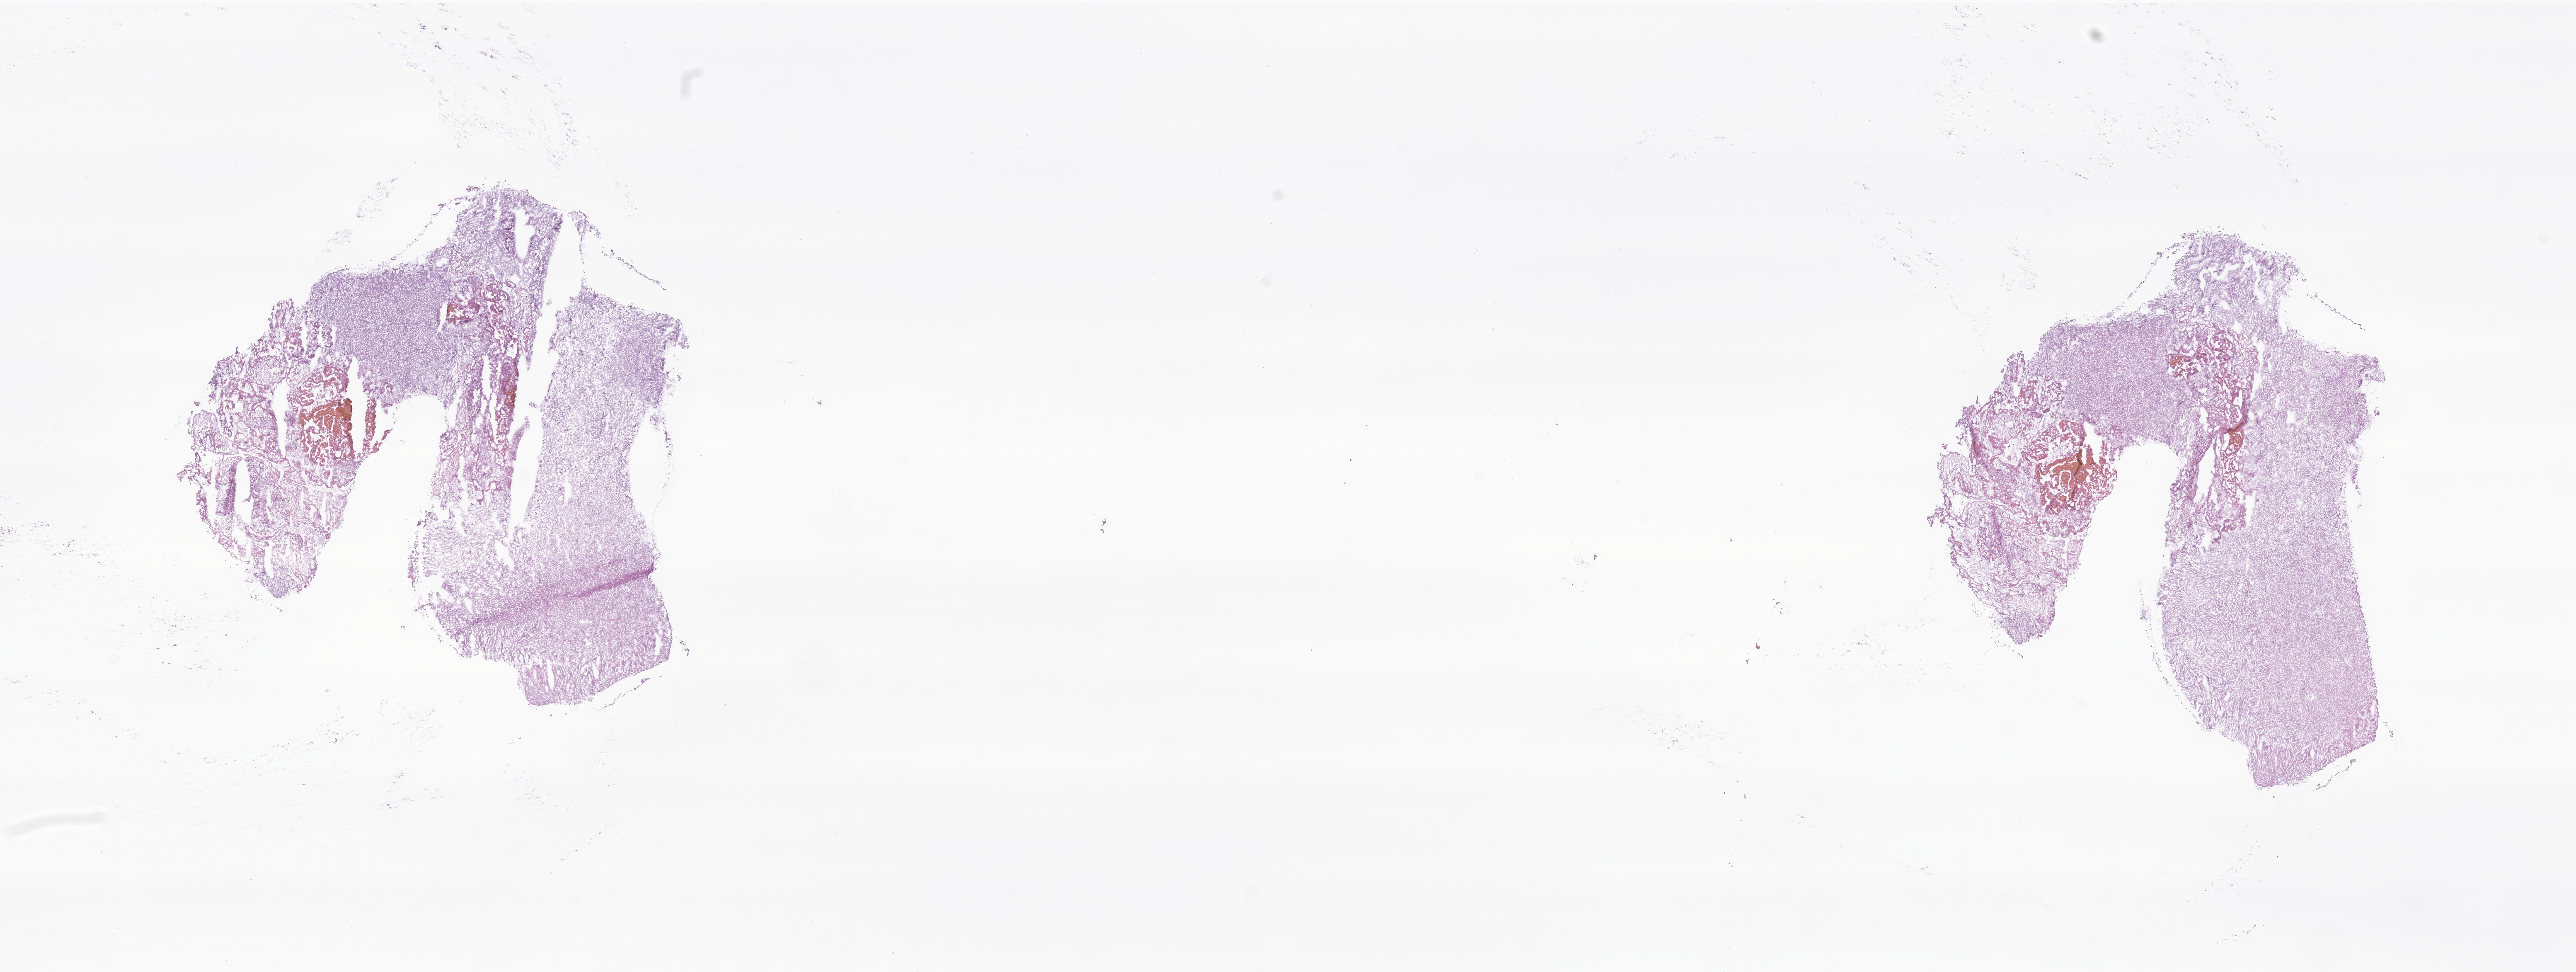
Whole-slide image, H&E stain of tumor tissue from the brain, a low-resolution overview of the entire scanned area, about 26.2 x 9.9 mm; cryosection (OCT / tissue freezing medium). Patient: male, age 124 months (10 years 4 months).
Diagnosis: Pilocytic astrocytoma.